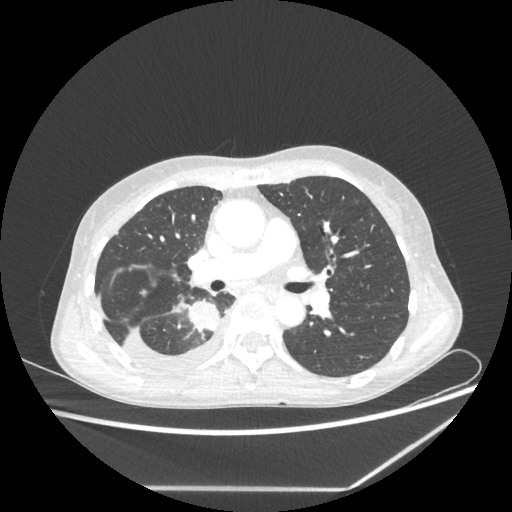
Chest CT, one axial slice. Slice 133 of 237 in the series (ordered by position). Reconstruction kernel STANDARD. 80 kVp. Lung window (W 1500 / L -600 HU). 1.25 mm slice thickness. 512 × 512 image matrix, field of view 364 × 364 mm. Patient: female, 59 years. Case-level facts recorded for this patient, not image findings: clinical TNM (as recorded): T1c N1 M1.
Annotated regions visible in this slice (bounding box drawn by a radiologist):
- lung tumour (recorded histology: adenocarcinoma): bounding box <184,300,225,337> (left, top, right, bottom; pixels)